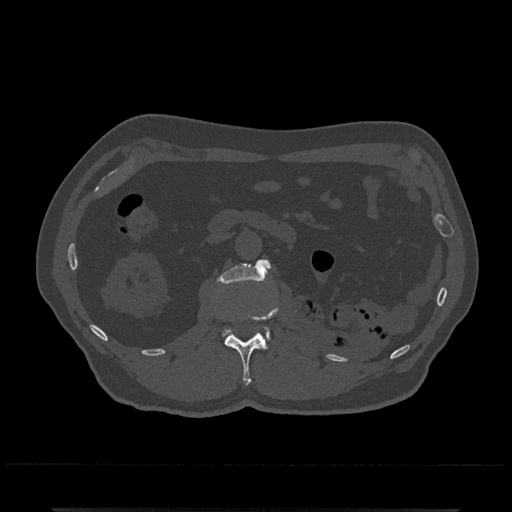
CT including the spine, one axial slice; position 335 of 797 along the scan axis; reconstruction kernel Br40s/3; 120 kVp; bone window (W 1800 / L 400 HU); 0.5 mm slice thickness; 512 × 512 image matrix, field of view 393 × 393 mm. Male patient, age 67 years. Case-level facts recorded for this patient, not image findings: primary cancer: prostate.
Structures marked on this image (semi-automatically segmented with operator editing):
- L1 vertebra: bounding box (x1, y1, x2, y2) in pixels: (225, 307, 278, 384)
- L2 vertebra: (217, 259, 271, 341)